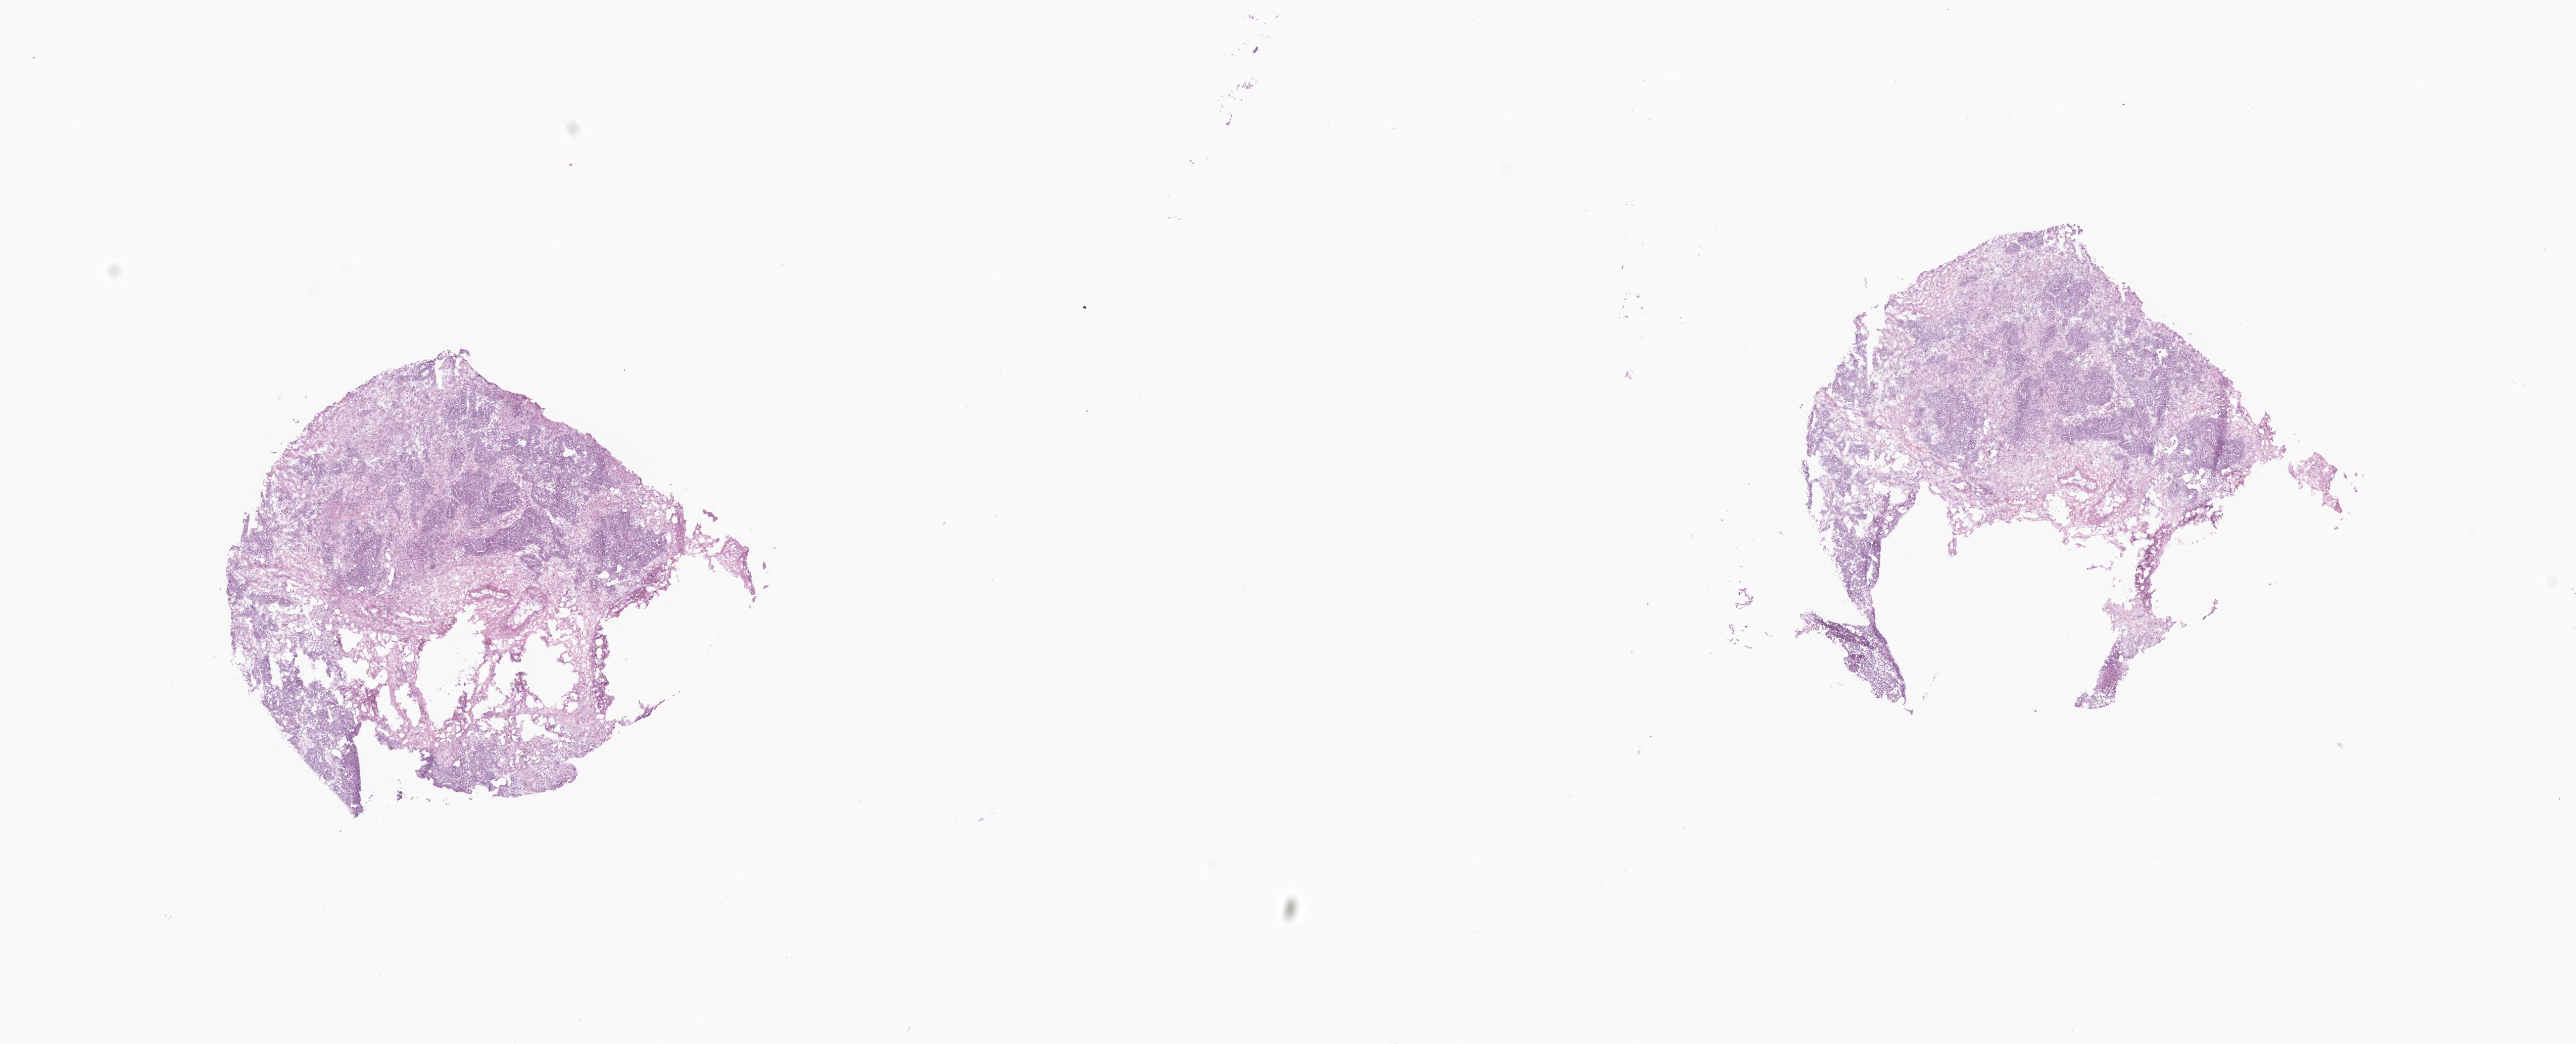
Digitized H&E-stained section, whole scanned area (about 21.5 x 8.7 mm) shown as a low-resolution overview. Cryosection. Specimen: metastatic tumor tissue, resected from specified parts of peritoneum. Female, age 62 years at initial diagnosis. Slide review estimates, as recorded: tumor cells 40%, tumor nuclei 40%, stromal cells 45%, necrosis 0%, normal cells 15%. Inflammatory infiltration, as recorded: lymphocyte infiltration 10%, monocyte infiltration 2%, neutrophil infiltration 0%.
Patient diagnosis (primary): Carcinoma, metastatic, NOS. Section: top of the tissue portion.